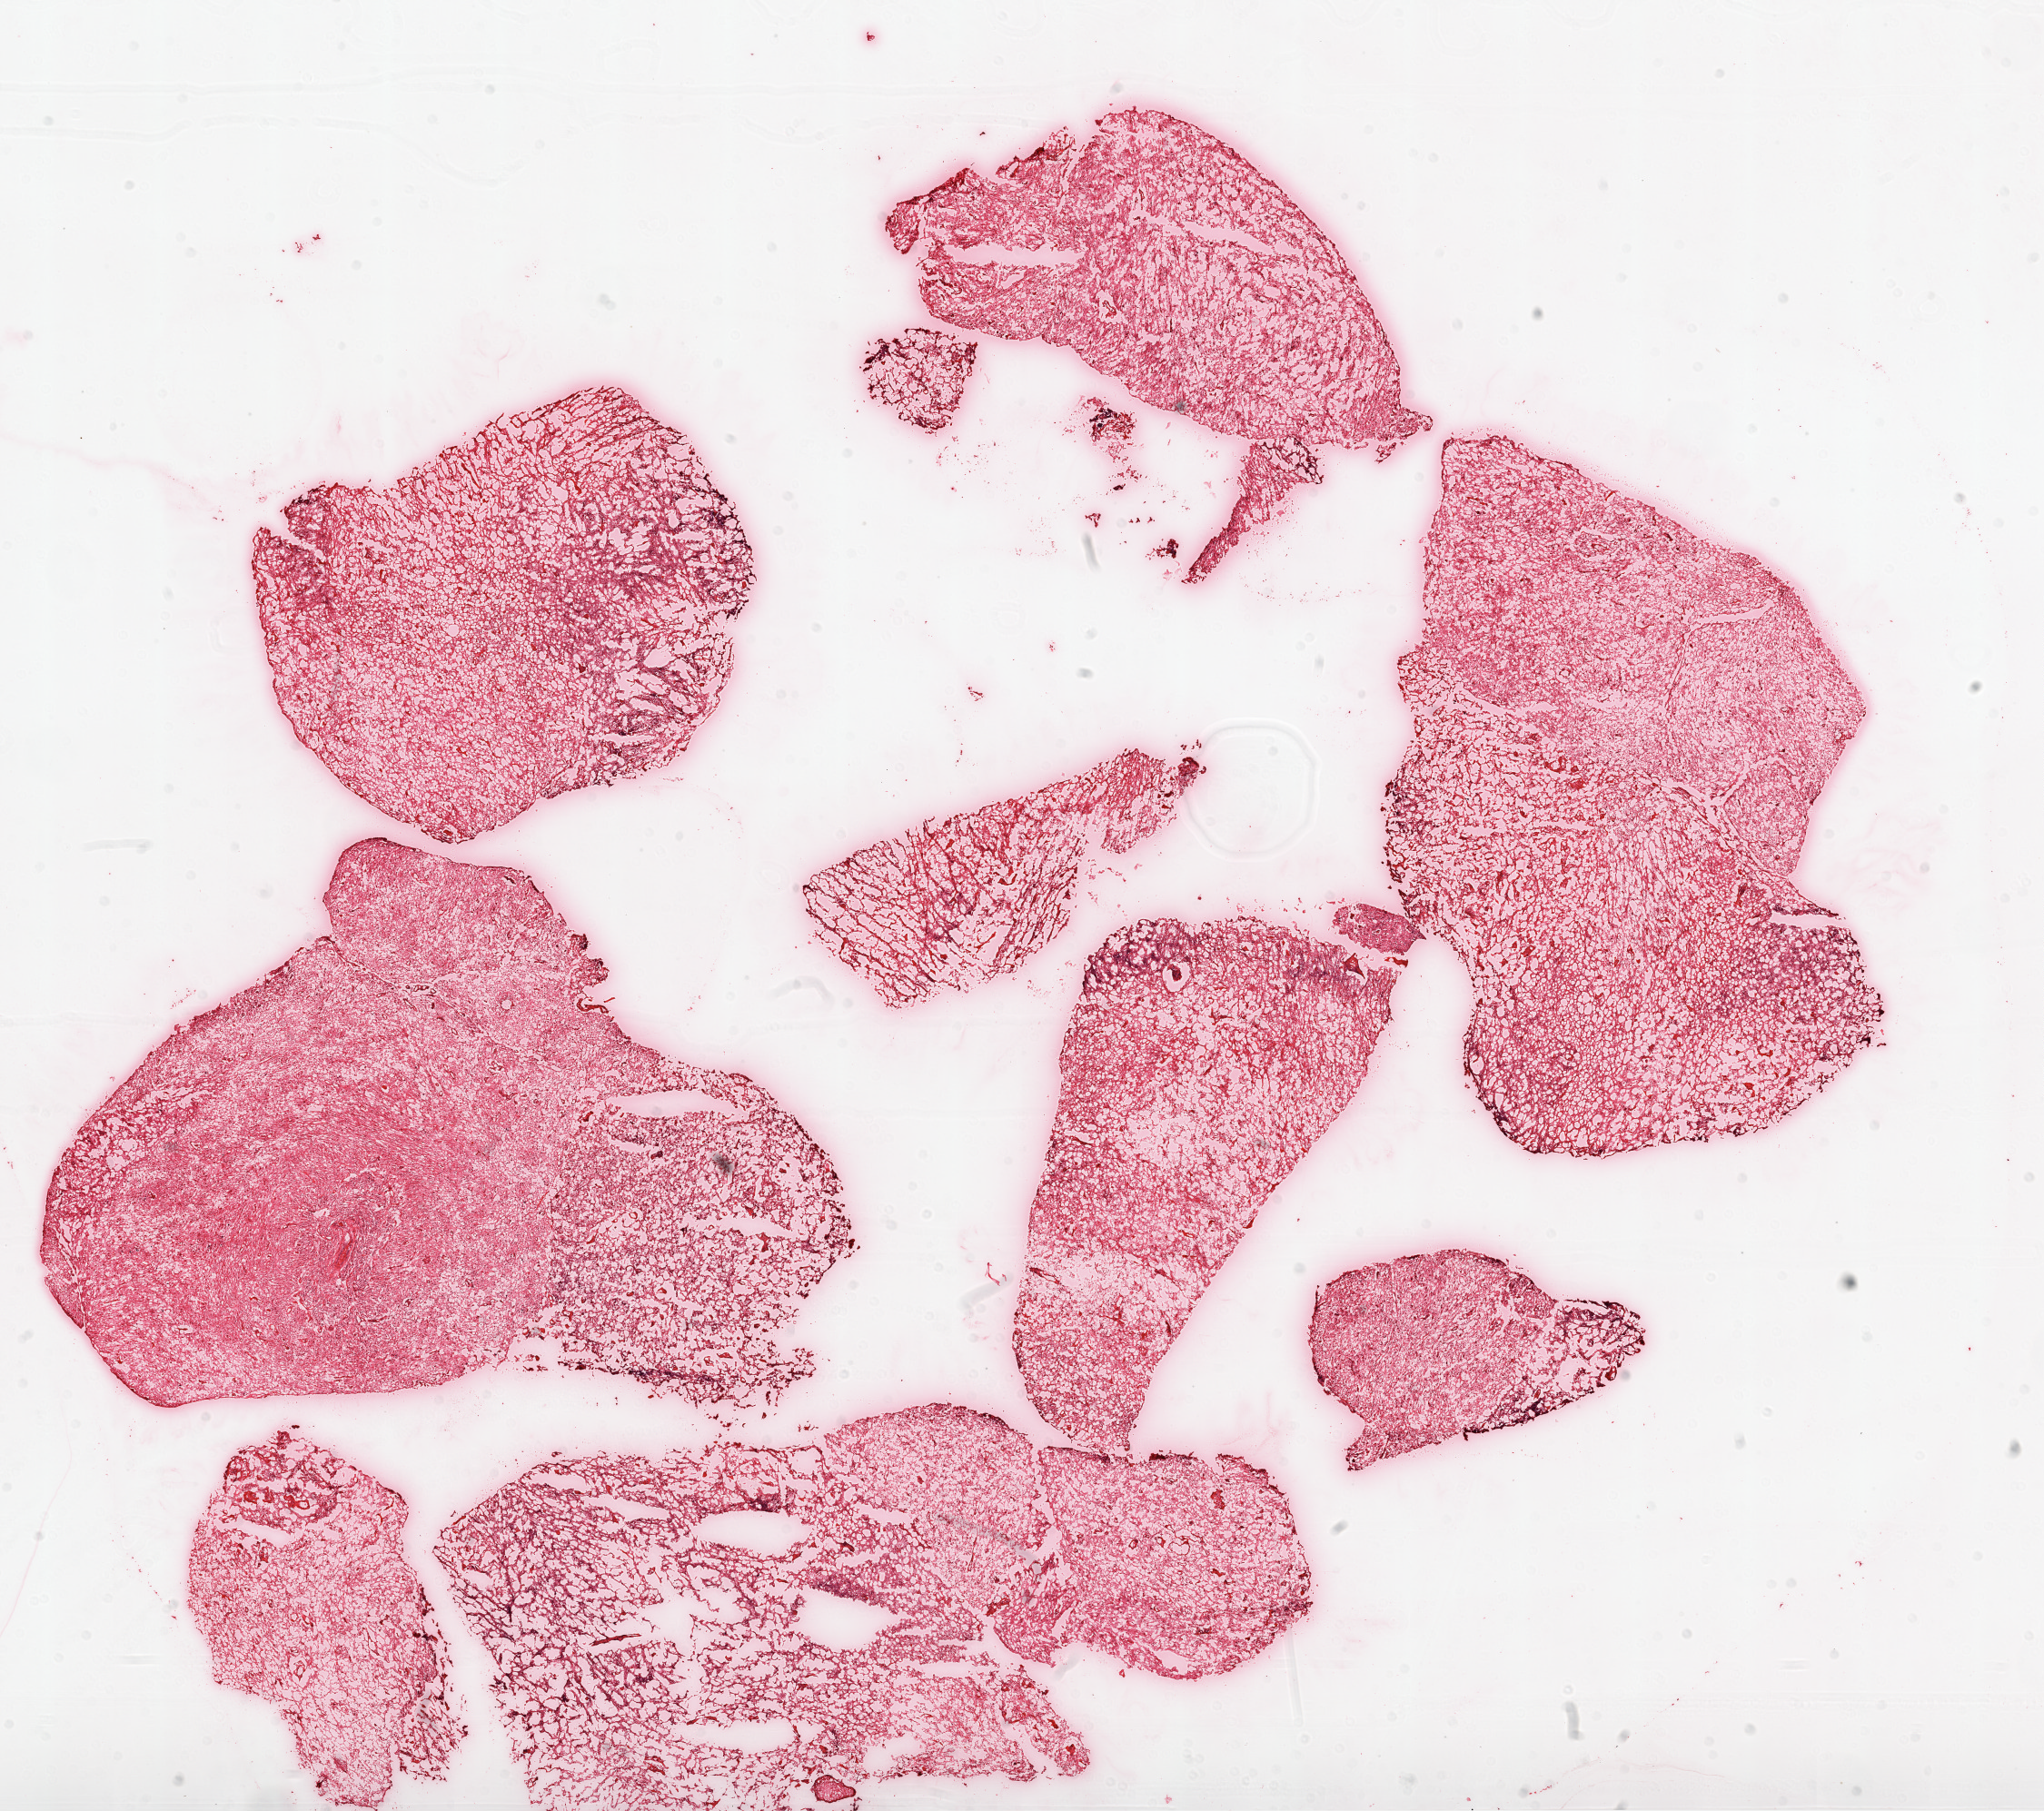
Digitized Hematoxylin and eosin (H&E) stained tissue section (whole slide) — whole scanned area (about 18.1 x 16.0 mm) shown as a low-resolution overview. Frozen section from the top of the tissue portion. Primary tumour sample from the brain. Male, age 49 years at initial diagnosis. Pathologist review of this section (percent, as recorded): tumour cells 90%, tumour nuclei 100%, normal cells 0%, stromal cells 0%, necrosis 10%.
Diagnosis: Glioblastoma.